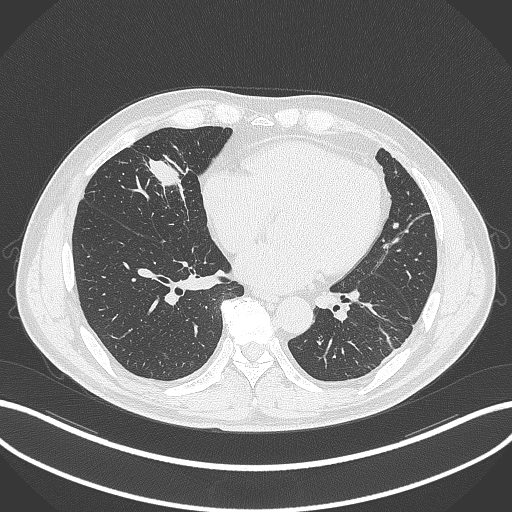
Chest CT, one axial slice; position 105 of 399 along the scan axis; lung window (W 1500 / L -600 HU); 512 × 512 image matrix, field of view 400 × 400 mm. Patient: male, 59 years. Case-level facts recorded for this patient, not image findings: clinical TNM (as recorded): T2a N1 M0.
Structures marked on this image (rectangle marked by the reading radiologist):
- lung tumour (recorded histology: adenocarcinoma): bounding box <140,146,192,195> (left, top, right, bottom; pixels)